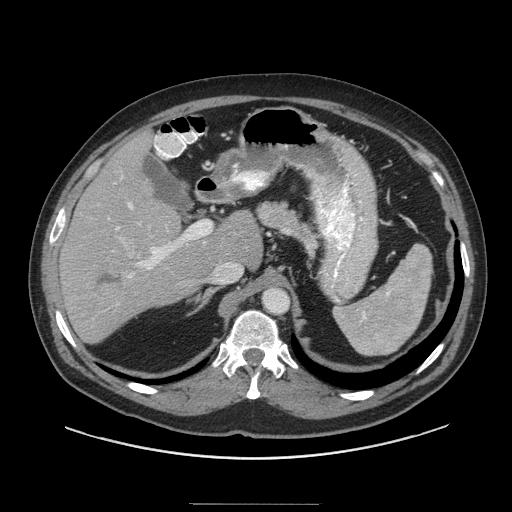
Contrast-enhanced abdominal CT (liver protocol), one axial slice; slice 61 of 91 in the series (ordered by position); reconstruction kernel STANDARD; soft-tissue window (W 400 / L 40 HU); 512 × 512 image matrix, field of view 440 × 440 mm. Case-level facts recorded for this patient, not image findings: diagnosis: hepatocellular carcinoma (patient treated with transarterial chemoembolisation; whether this scan precedes or follows treatment is not stated here); TNM stage (as recorded): Stage-I; Child-Pugh class: A; tumour nodularity: uninodular.
Outlined on this slice (semi-automatic segmentation, software-assisted and operator-edited):
- liver parenchyma outside the tumour (the mass and vessels are separate outlines, so this box may not span the whole liver): box from (x=58, y=132) to (x=262, y=342) px
- mass: (x=90, y=269)–(x=126, y=298)
- liver vessels: (x=108, y=176)–(x=242, y=278)